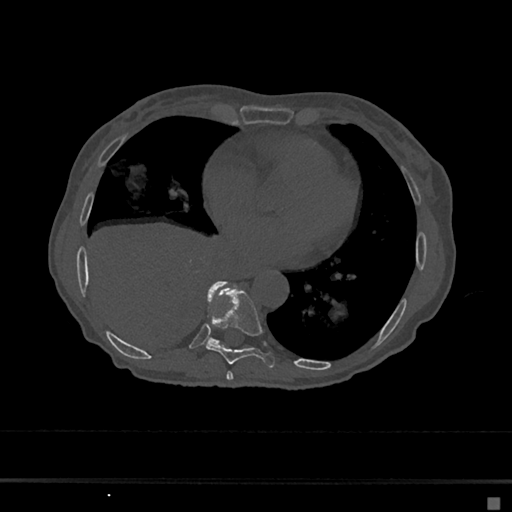
CT including the spine, one axial slice. Slice 313 of 797 in the series (ordered by position). Reconstruction kernel Br40s/3. Bone window (W 1800 / L 400 HU). 0.5 mm slice thickness. 512 × 512 image matrix. Female patient, age 68 years. Case-level facts recorded for this patient, not image findings: primary cancer: renal.
Outlined on this slice (semi-automatic segmentation, software-assisted and operator-edited):
- T7 vertebra: bounding box [x1, y1, x2, y2] px = [226, 371, 234, 381]
- T8 vertebra: [206, 288, 275, 368]
- T9 vertebra: [208, 281, 226, 344]